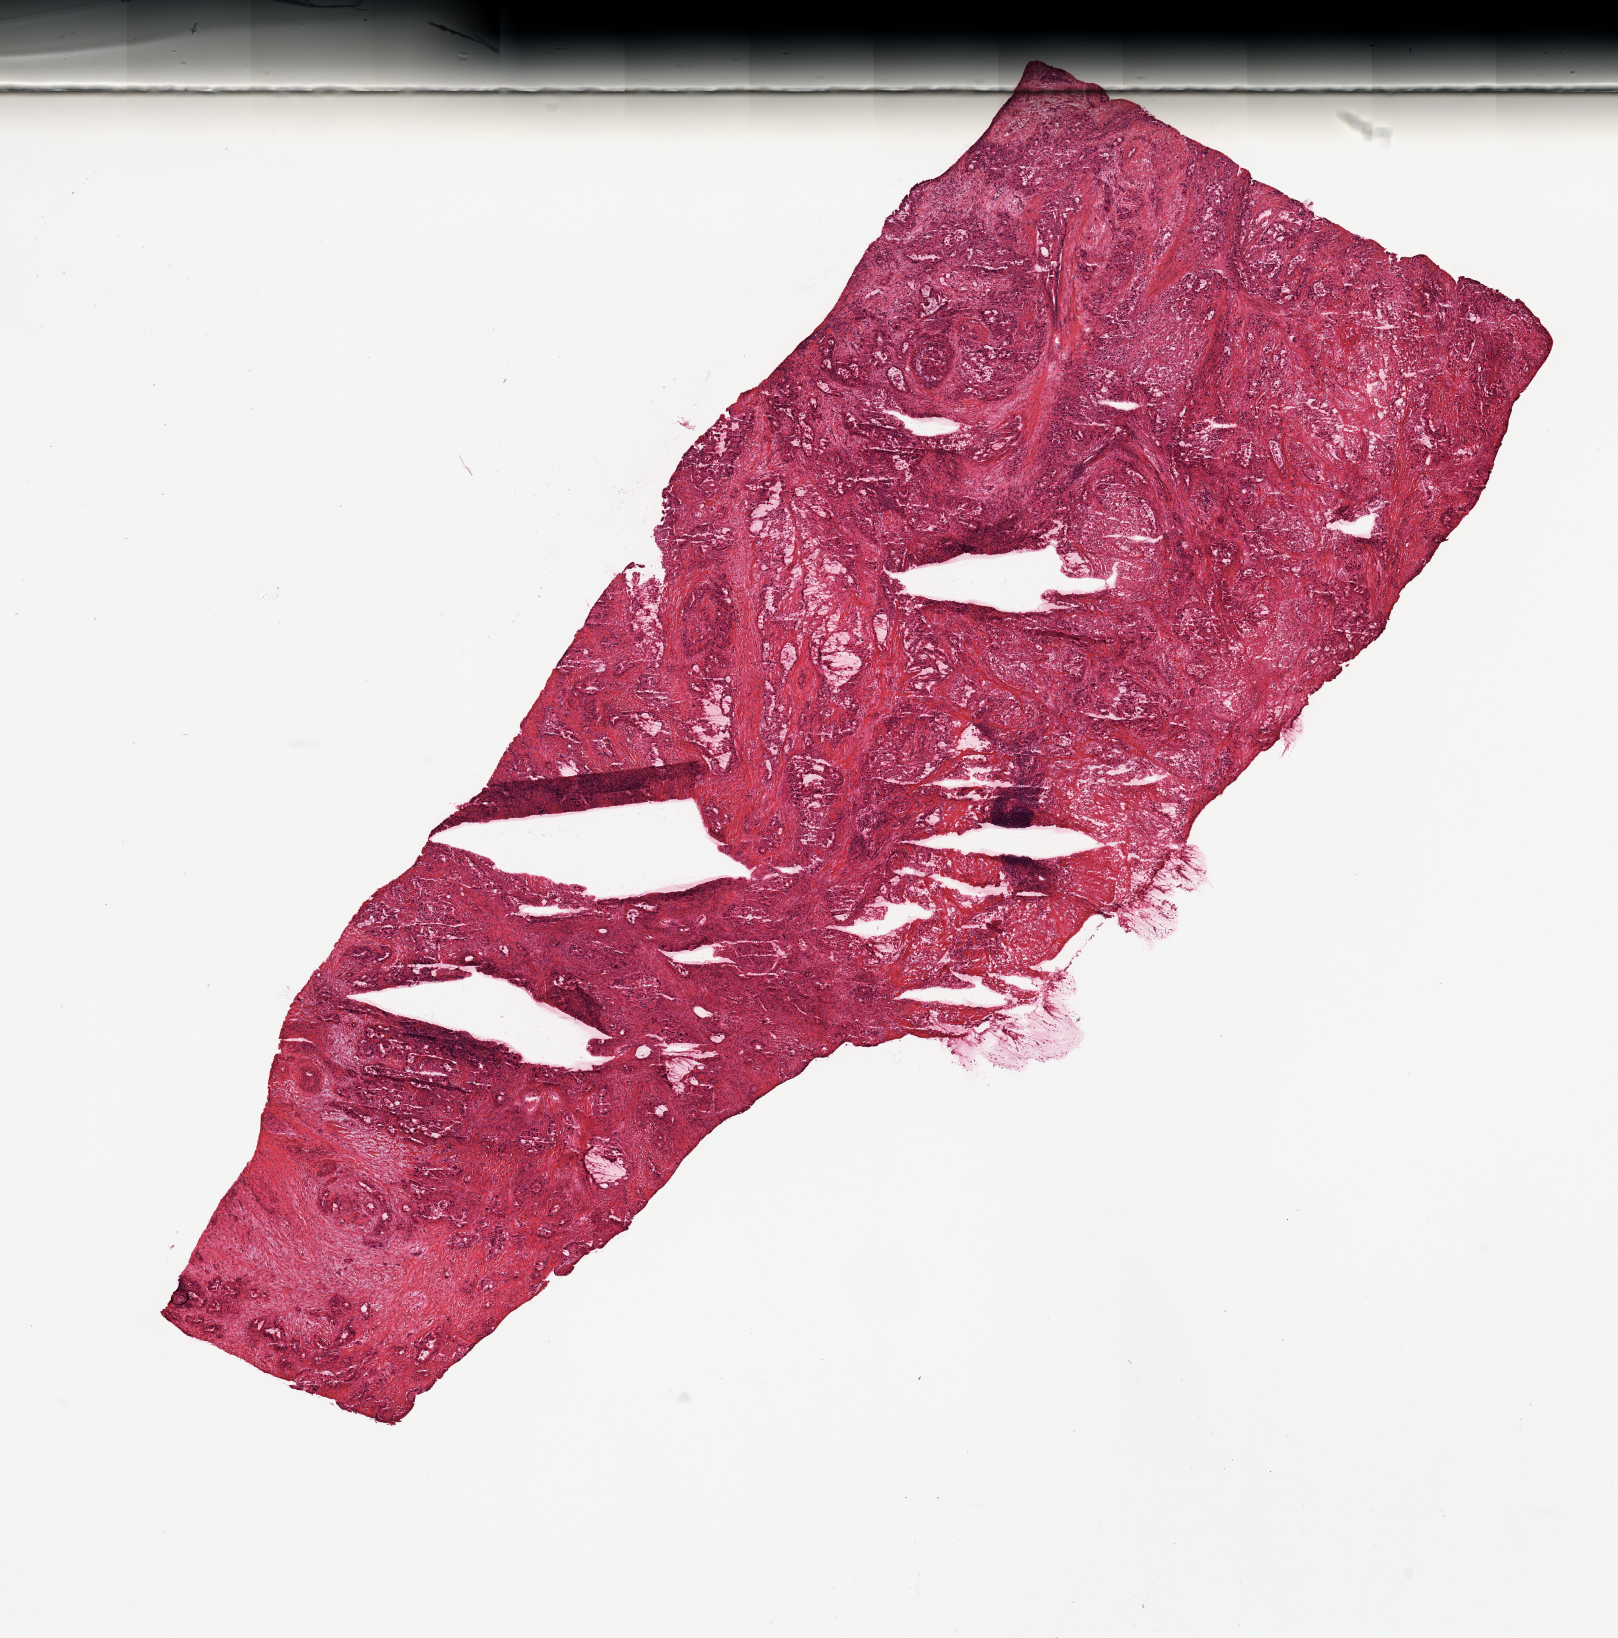
Digitized H&E tissue section (whole slide), whole scanned area (about 12.8 x 13.0 mm, slide scanned at 20x) shown as a low-resolution overview, tumour tissue sample, sampled site: pancreas. 61-year-old female patient. Histologic grade: G2 (moderately differentiated). Composition of this section per pathologist review: tumour nuclei 50%, necrosis 5%.
Histologic diagnosis: Infiltrating duct carcinoma, NOS. AJCC pathologic stage: IIB. Primary tumour site (as recorded): head.